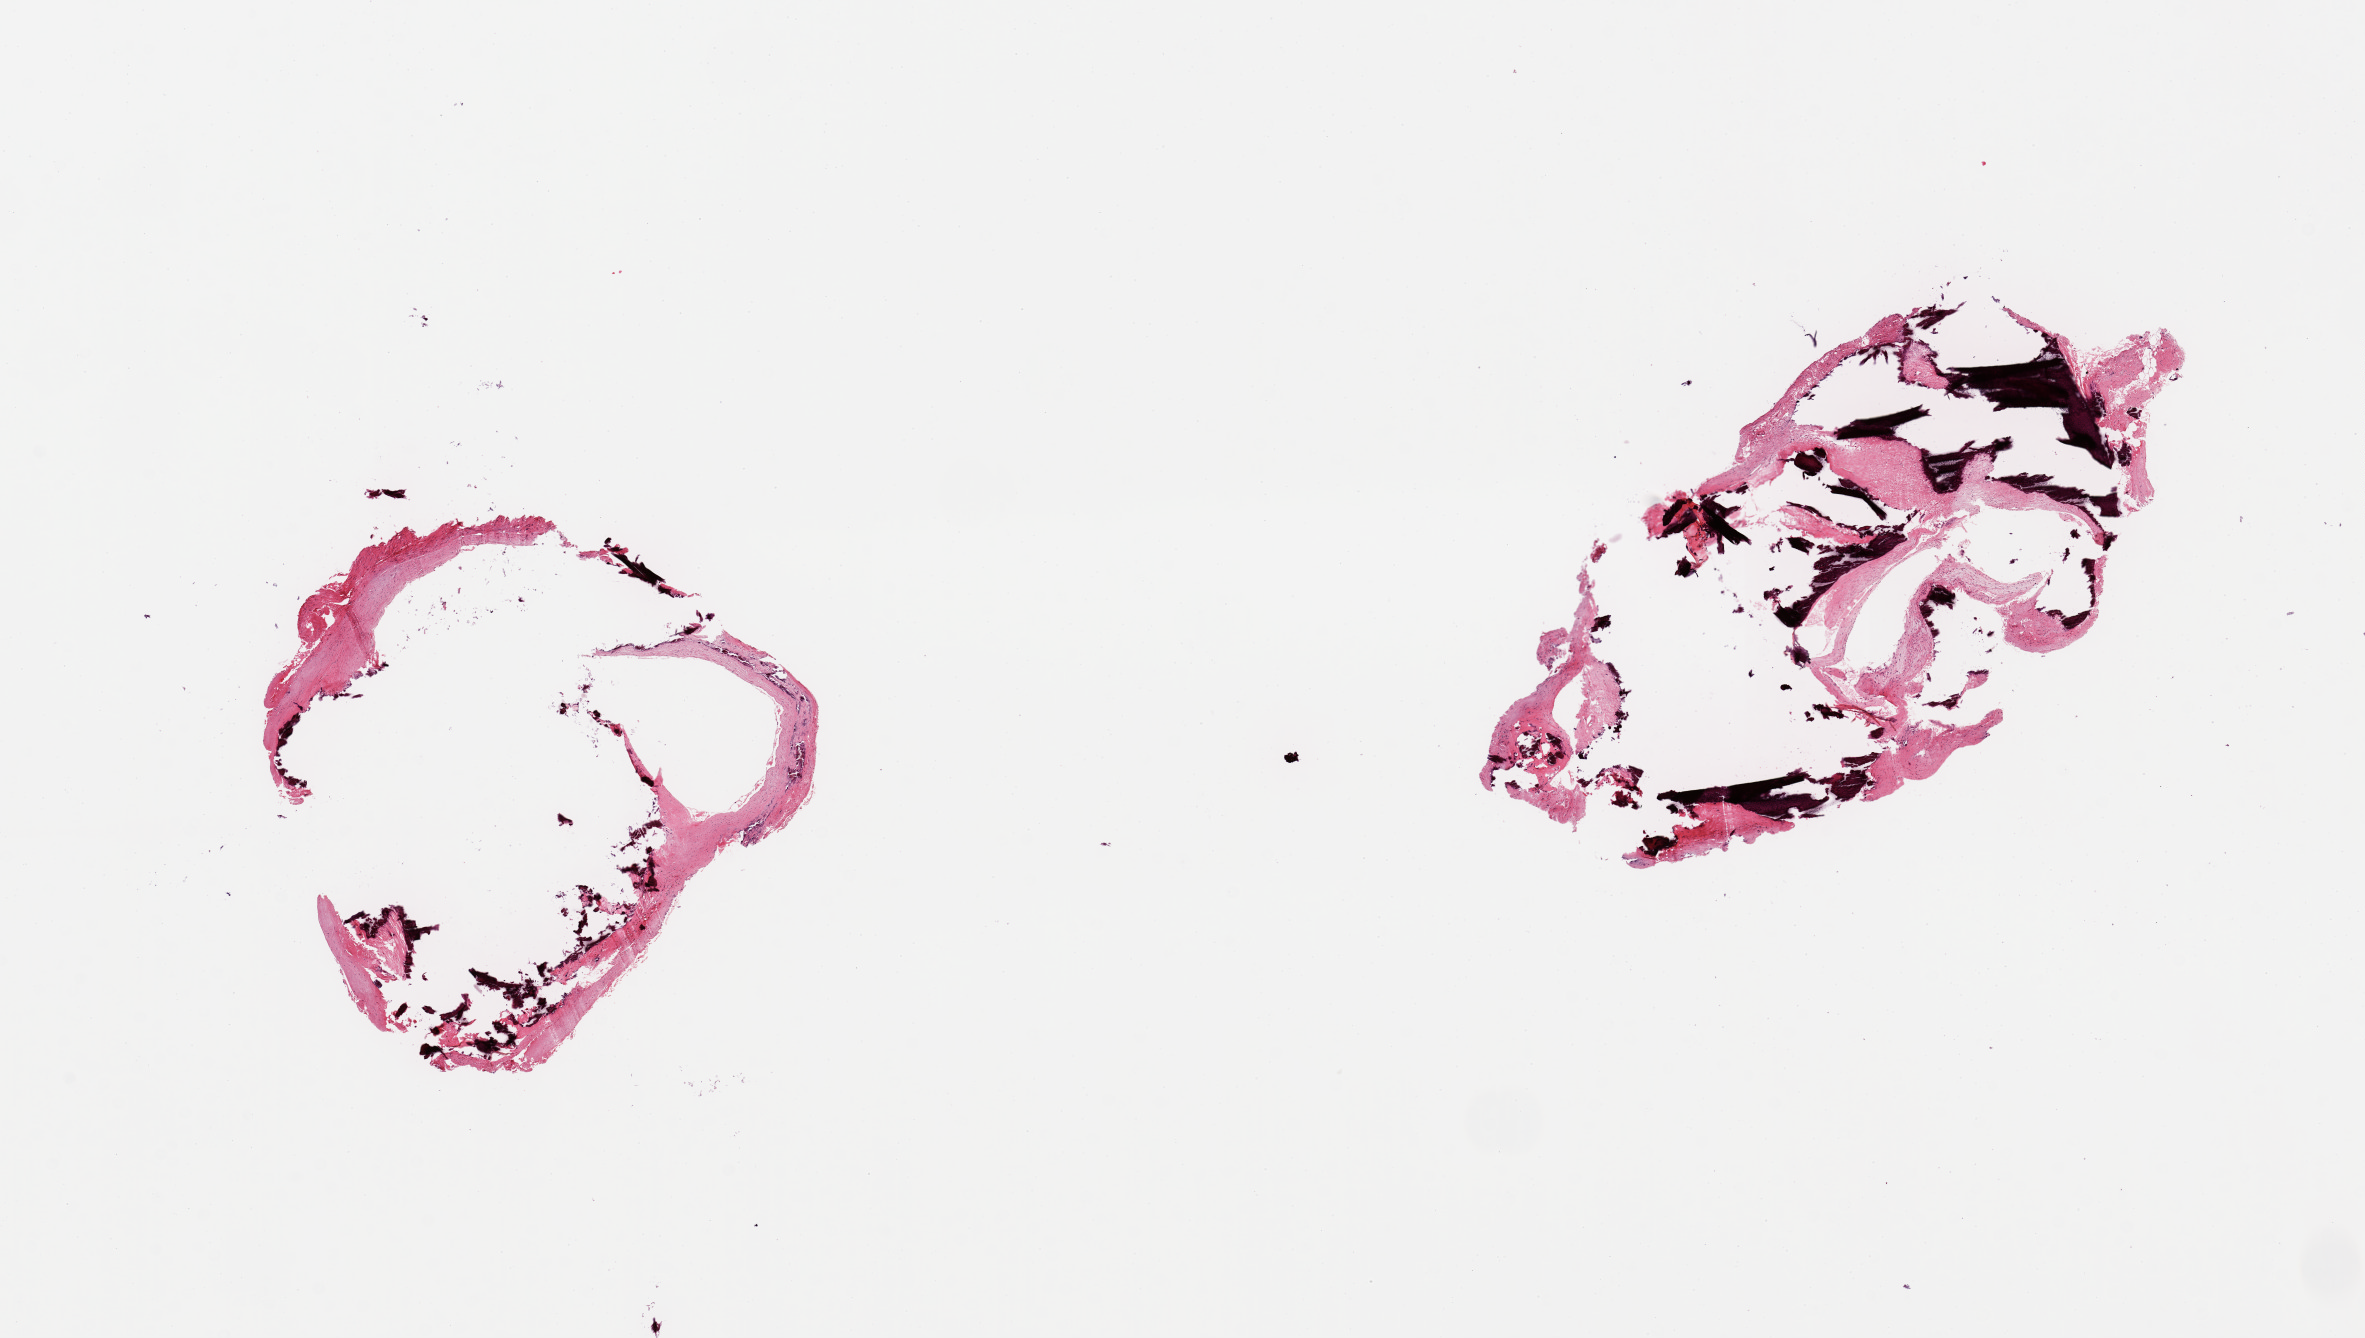
Whole-slide image, hematoxylin and eosin (H&E) stain, brightfield — low-resolution overview of the scanned area, about 18.7 x 10.6 mm (slide scanned at 20x). PAXgene-fixed paraffin-embedded (PFPE) section. Sampled site (target tissue): coronary artery. Tissue donor sample.
Reviewer comment on this tissue sample: 2 pieces, subtotally occlusive calcified atherosis.